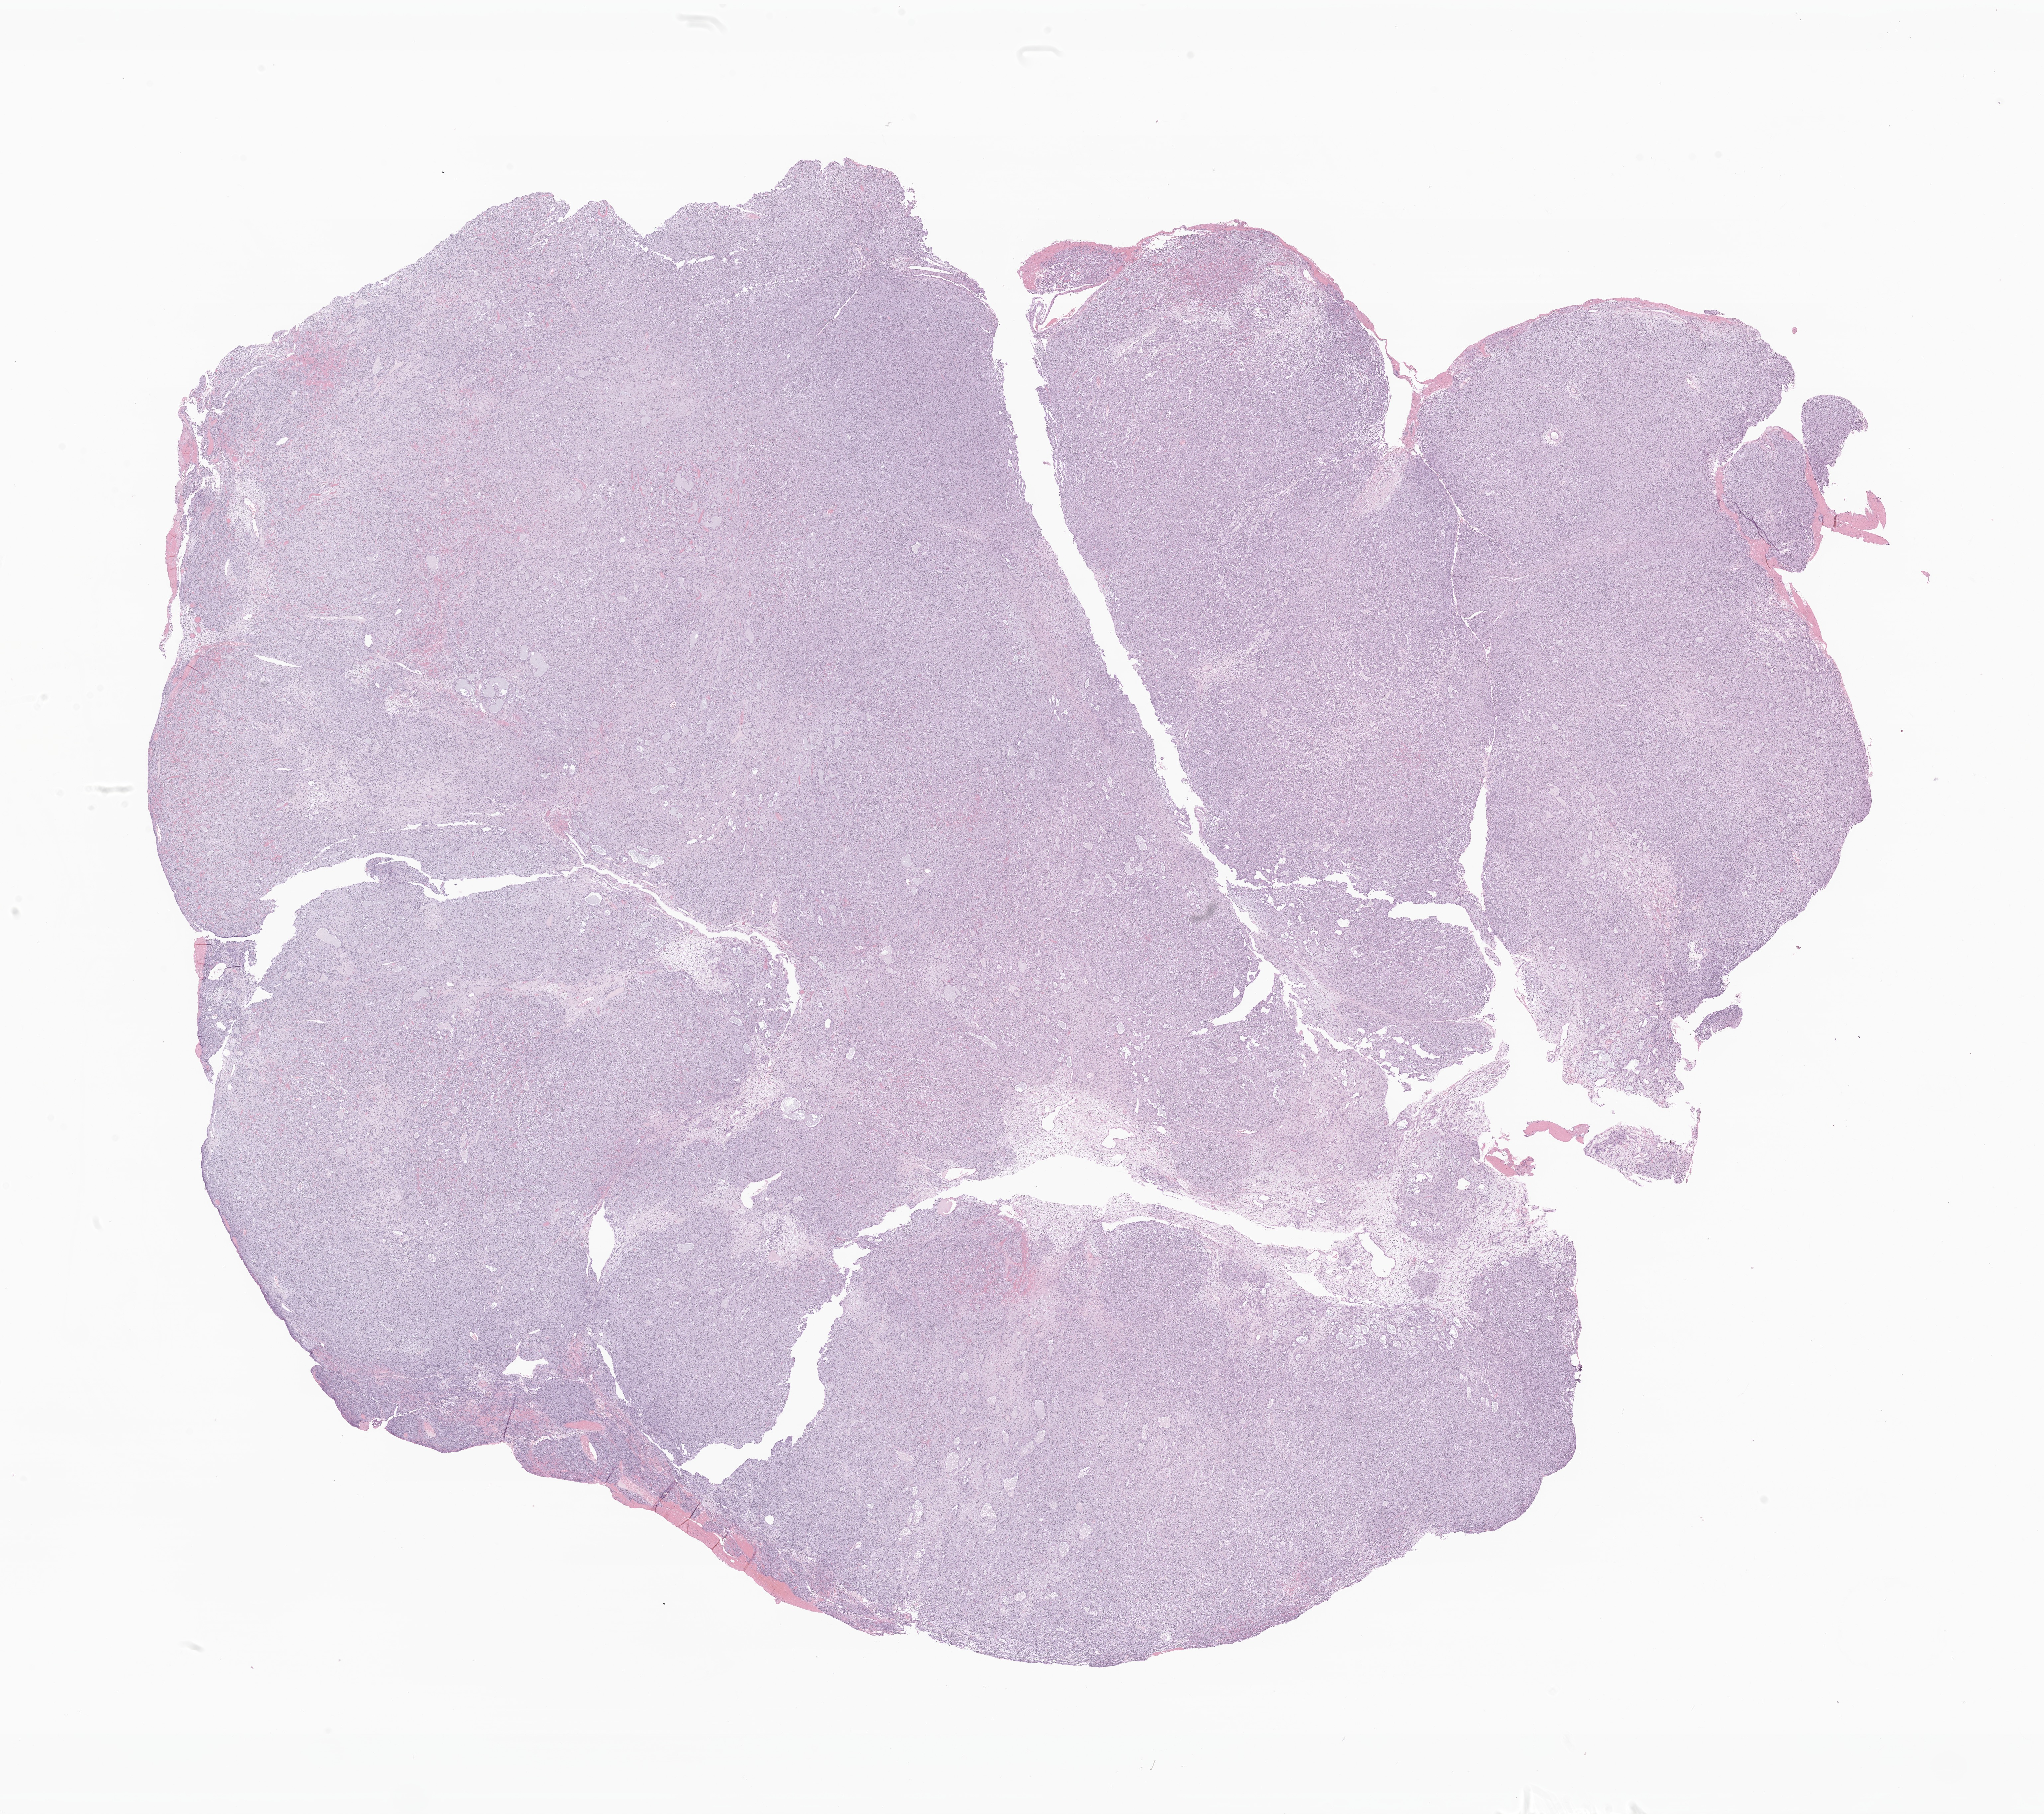
Haematoxylin and eosin whole-slide image of tumor tissue from the ovary, a low-resolution overview of the entire scanned area, about 25.9 x 23.0 mm; FFPE section. Patient female; age 204 months (17 years).
- diagnosis (ICD-O-3 morphology term): Granulosa cell tumor, juvenile